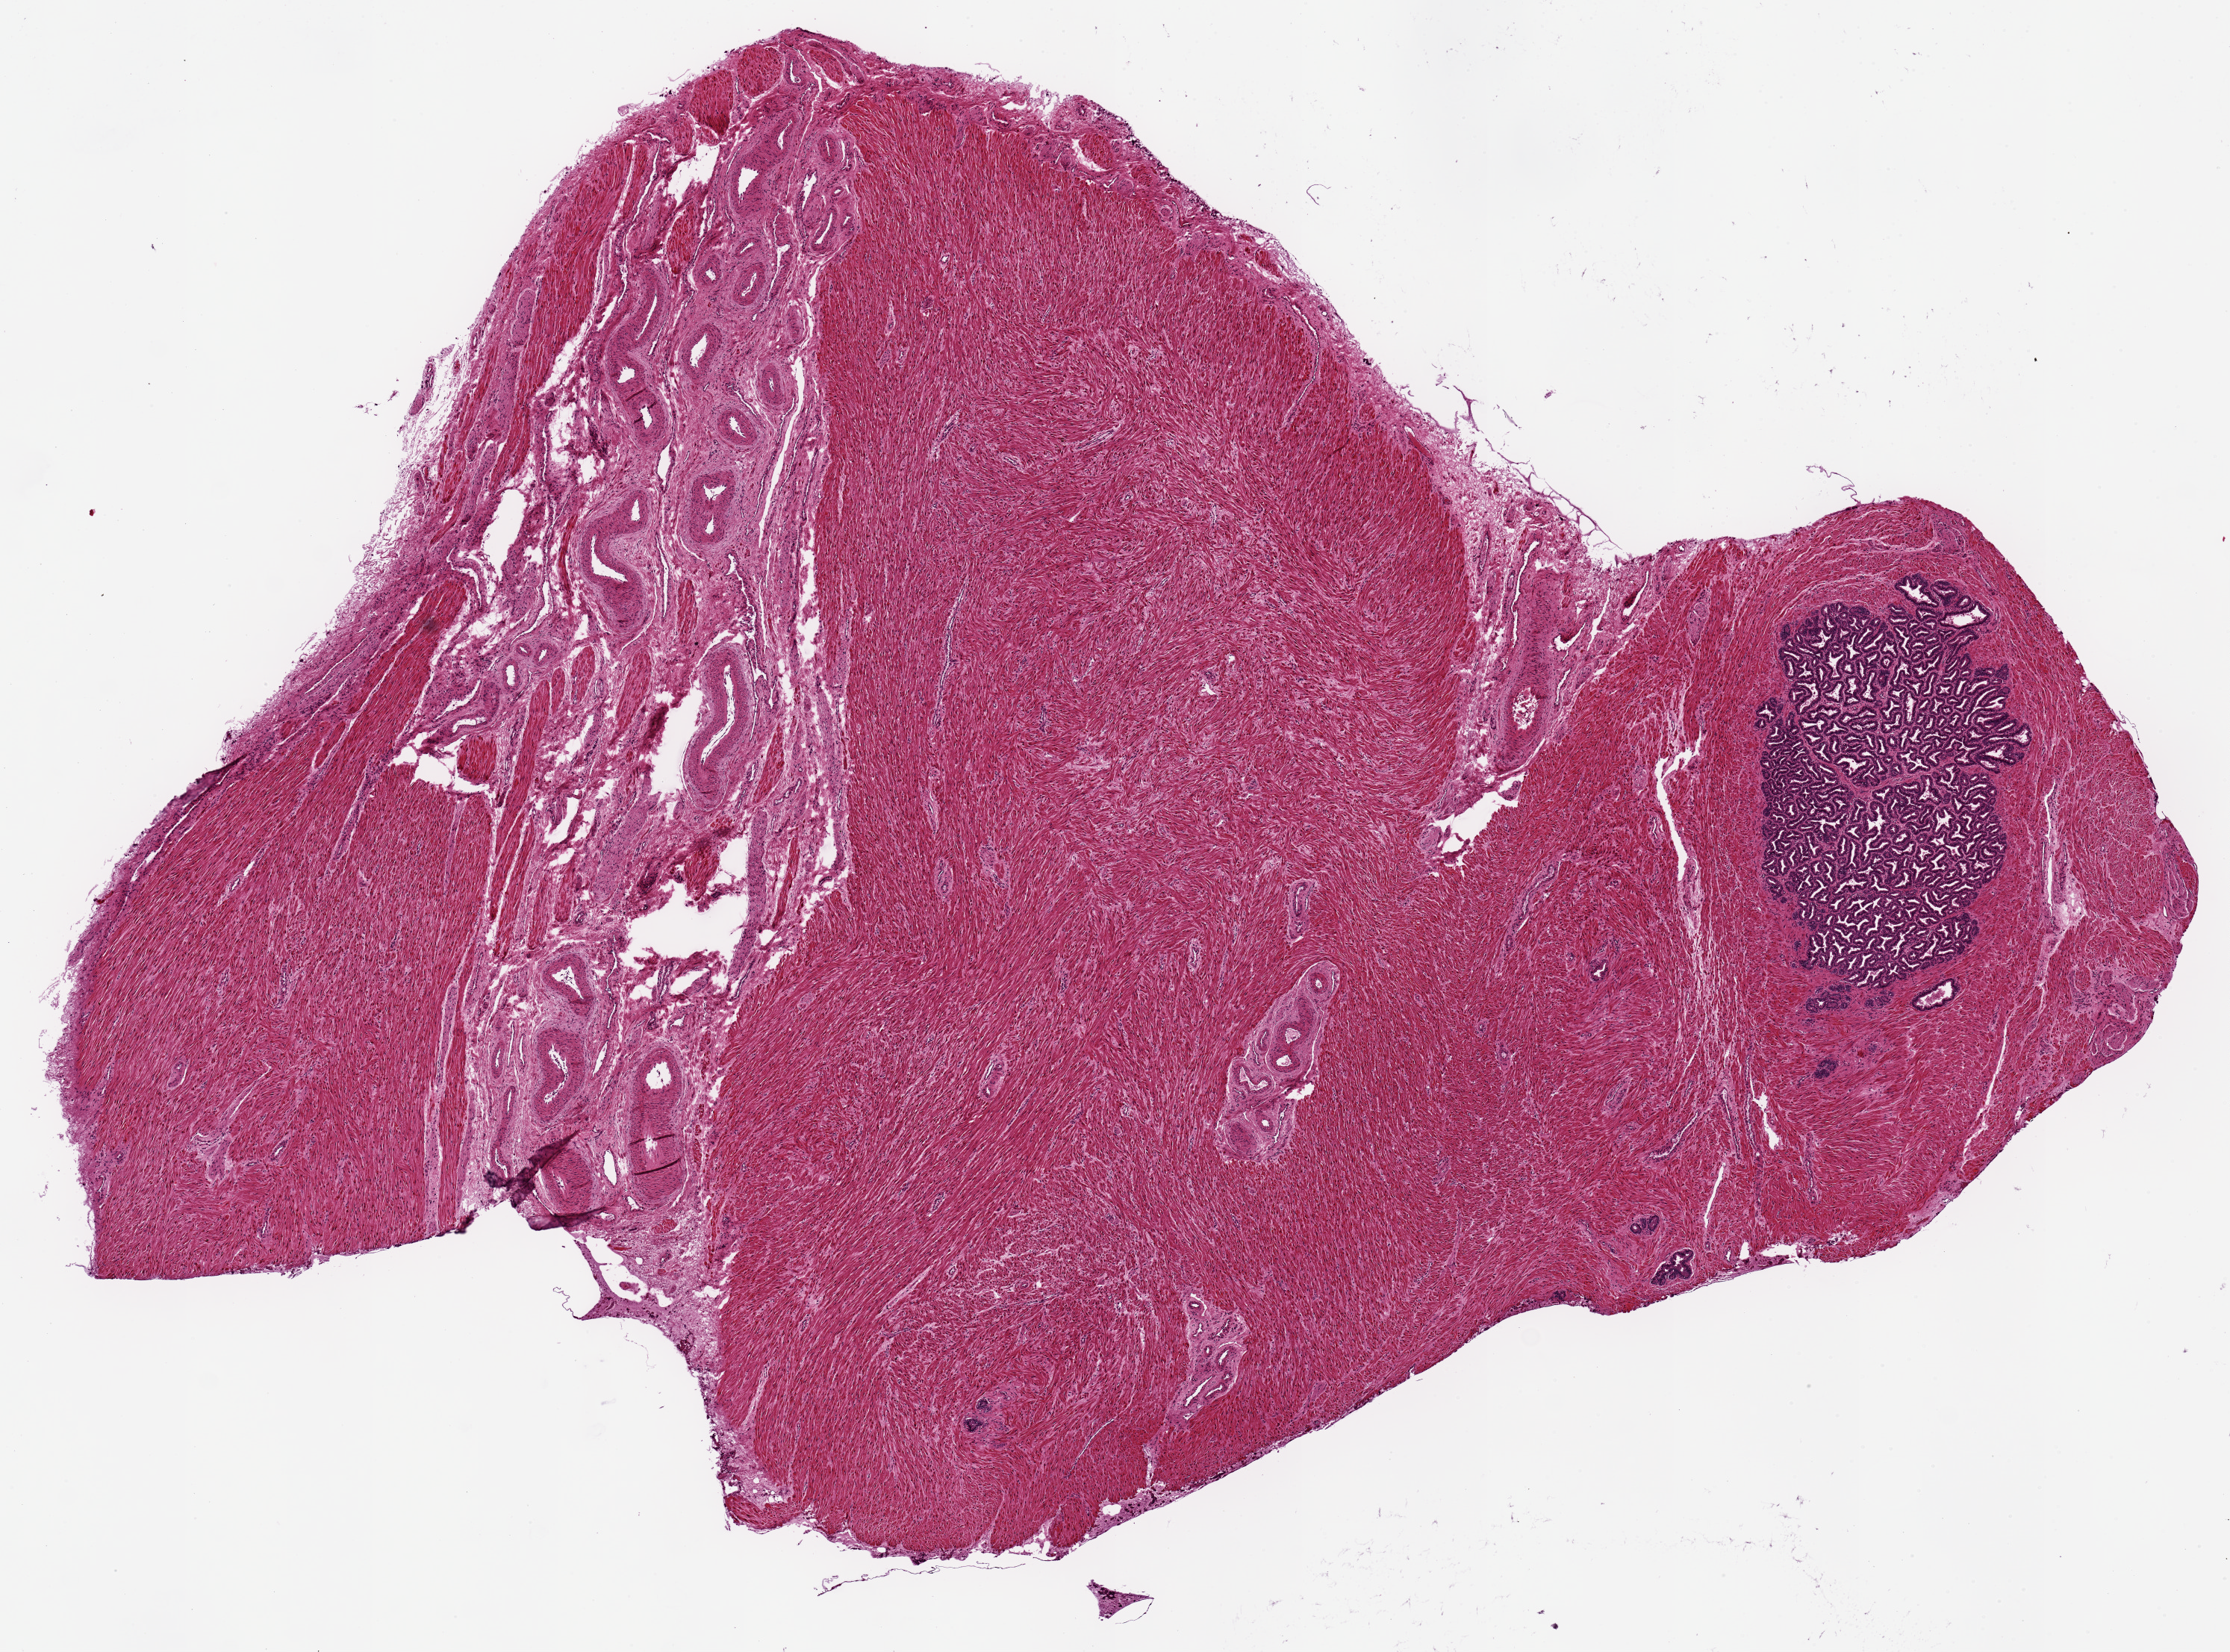
Whole-slide image, hematoxylin and eosin (H&E) stain — low-resolution overview of the scanned area, about 11.8 x 8.8 mm, PAXgene-fixed paraffin-embedded (PFPE) section, sampled site (target tissue): prostate, donor tissue sample.
Reviewer comment on this tissue sample: appears to be seminal vesicle, not prostate; glands = only 4% of aliquot.